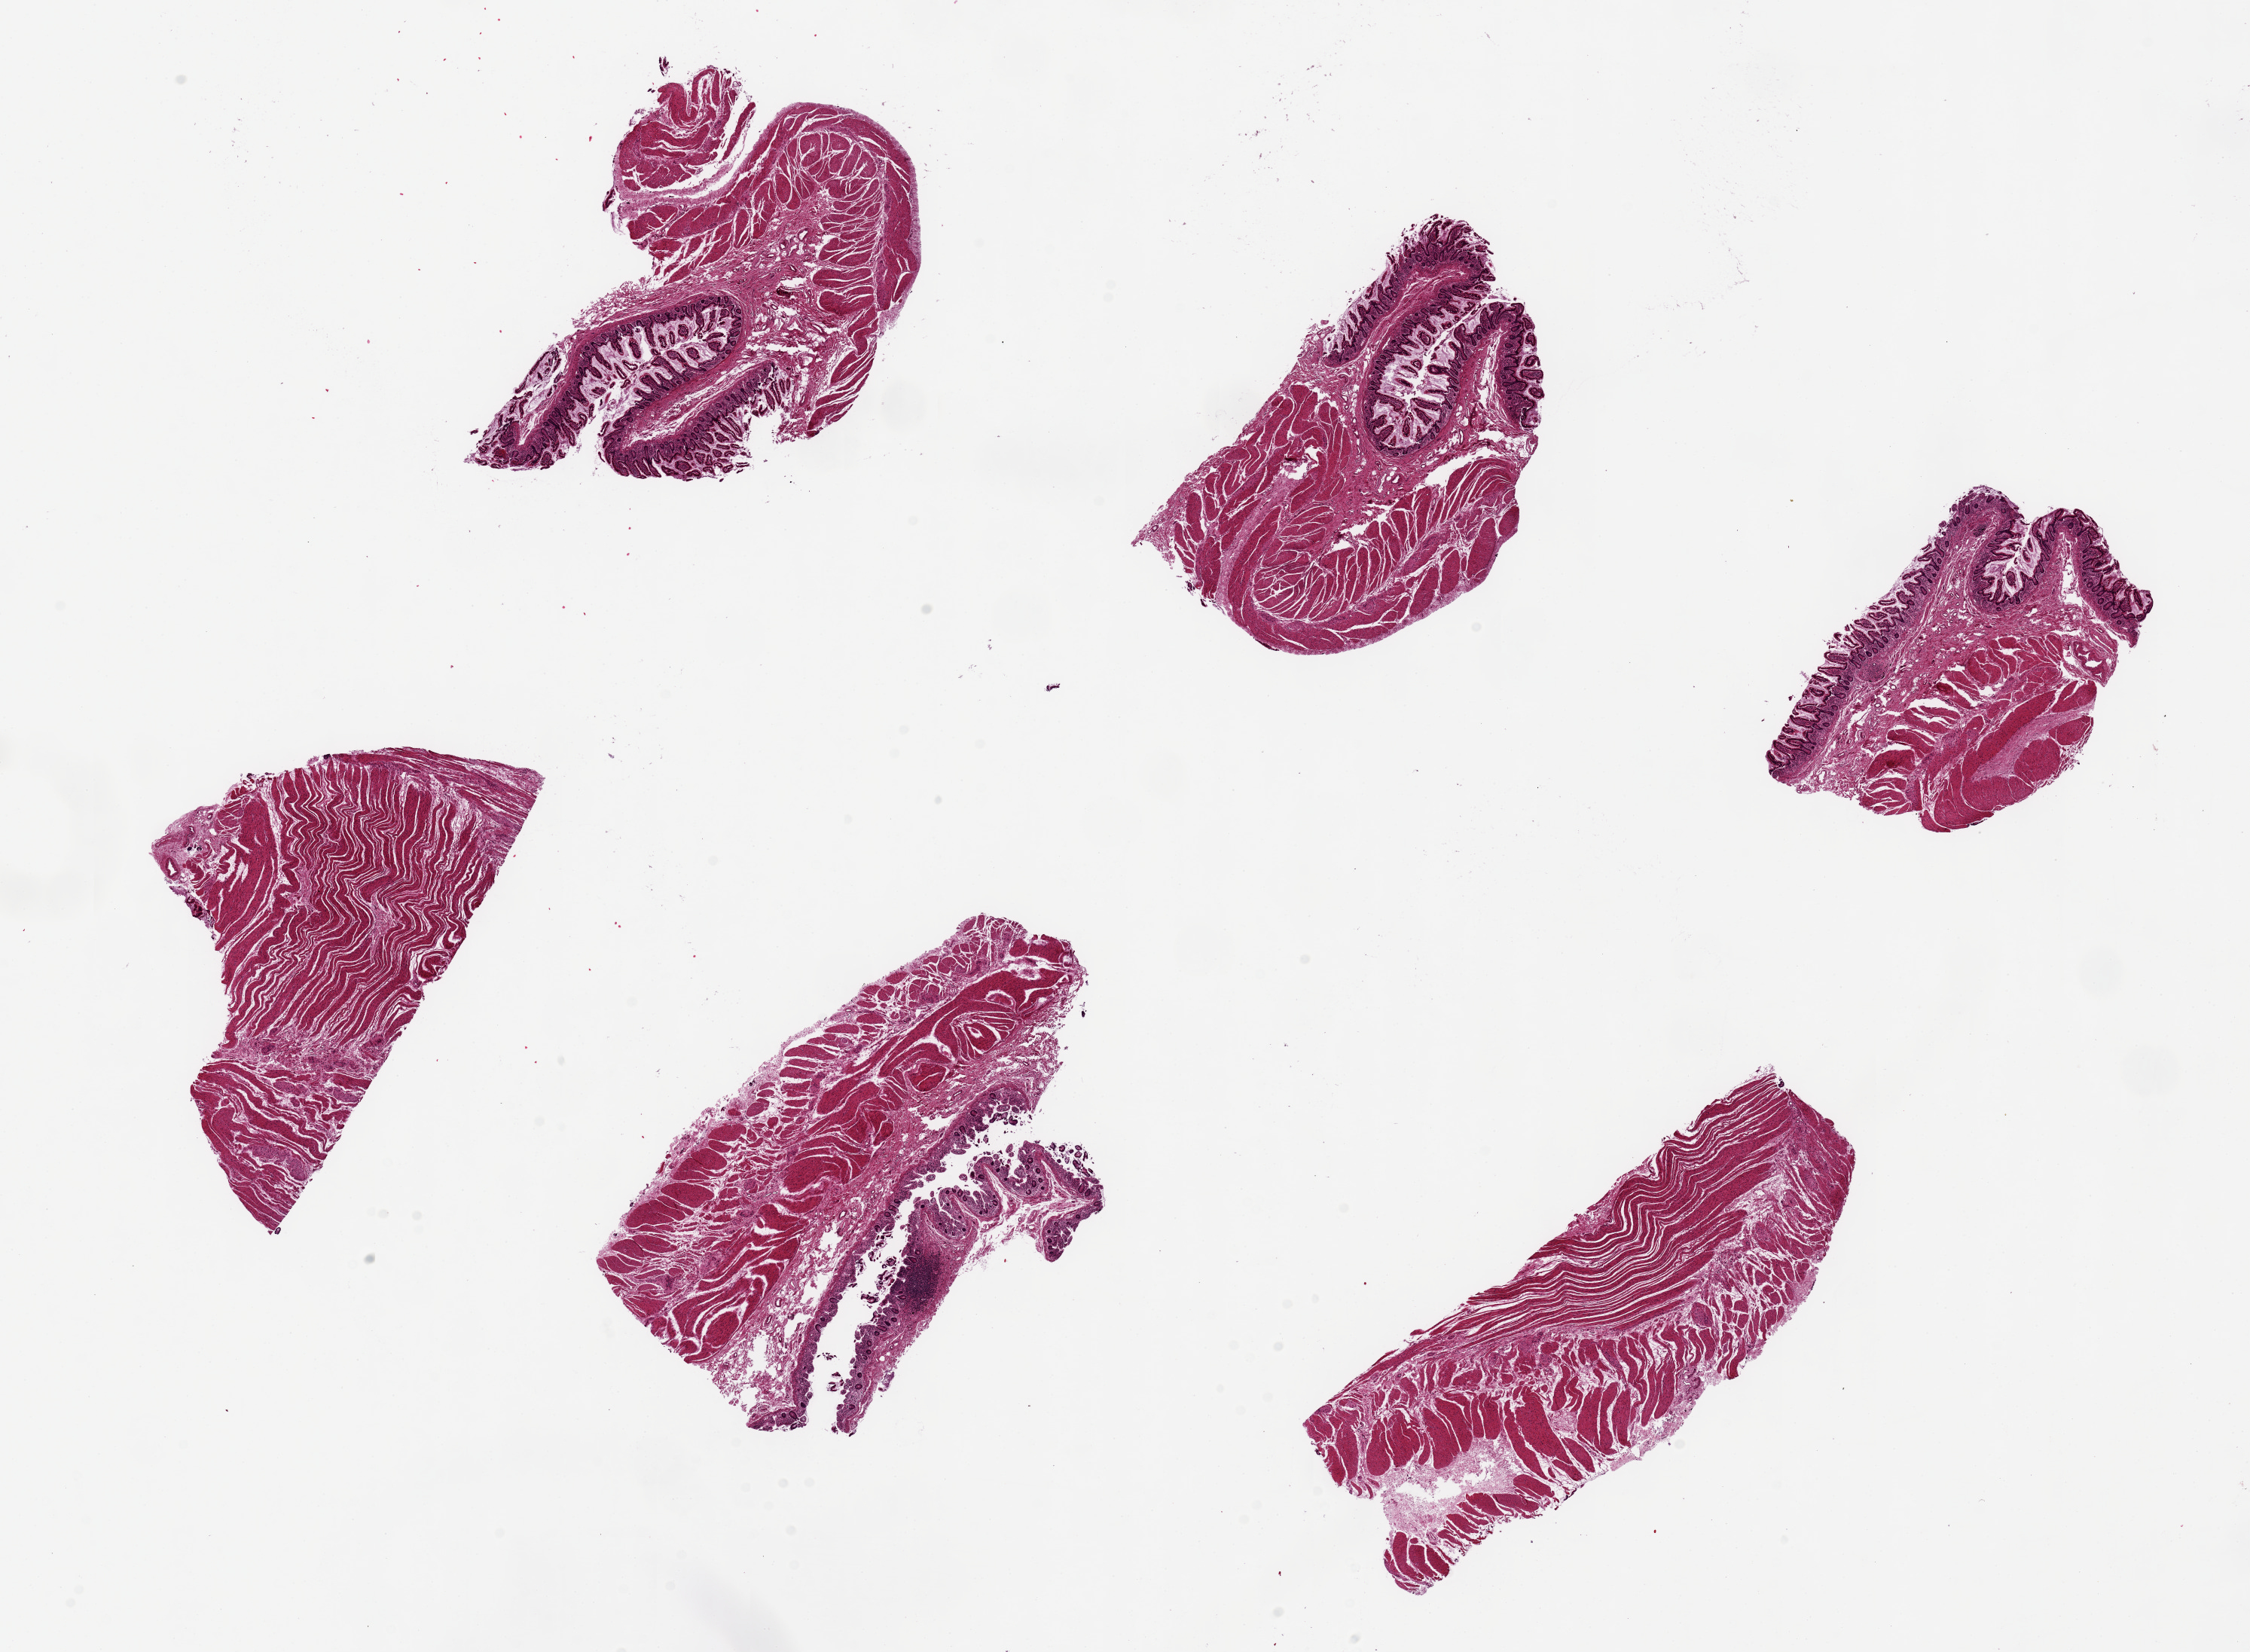
Whole-slide image, hematoxylin and eosin (H&E) stain, brightfield, a low-resolution overview of the entire scanned area, about 23.6 x 17.3 mm (acquisition: 20x scan); PAXgene-fixed paraffin-embedded (PFPE) section; section of ileum (target tissue); donor tissue sample.
Pathologist's review note for this sample: 6 pieces, up to 6.5x2.5mm; abundant mucosa, only focal lymphoid aggregates <5% total.